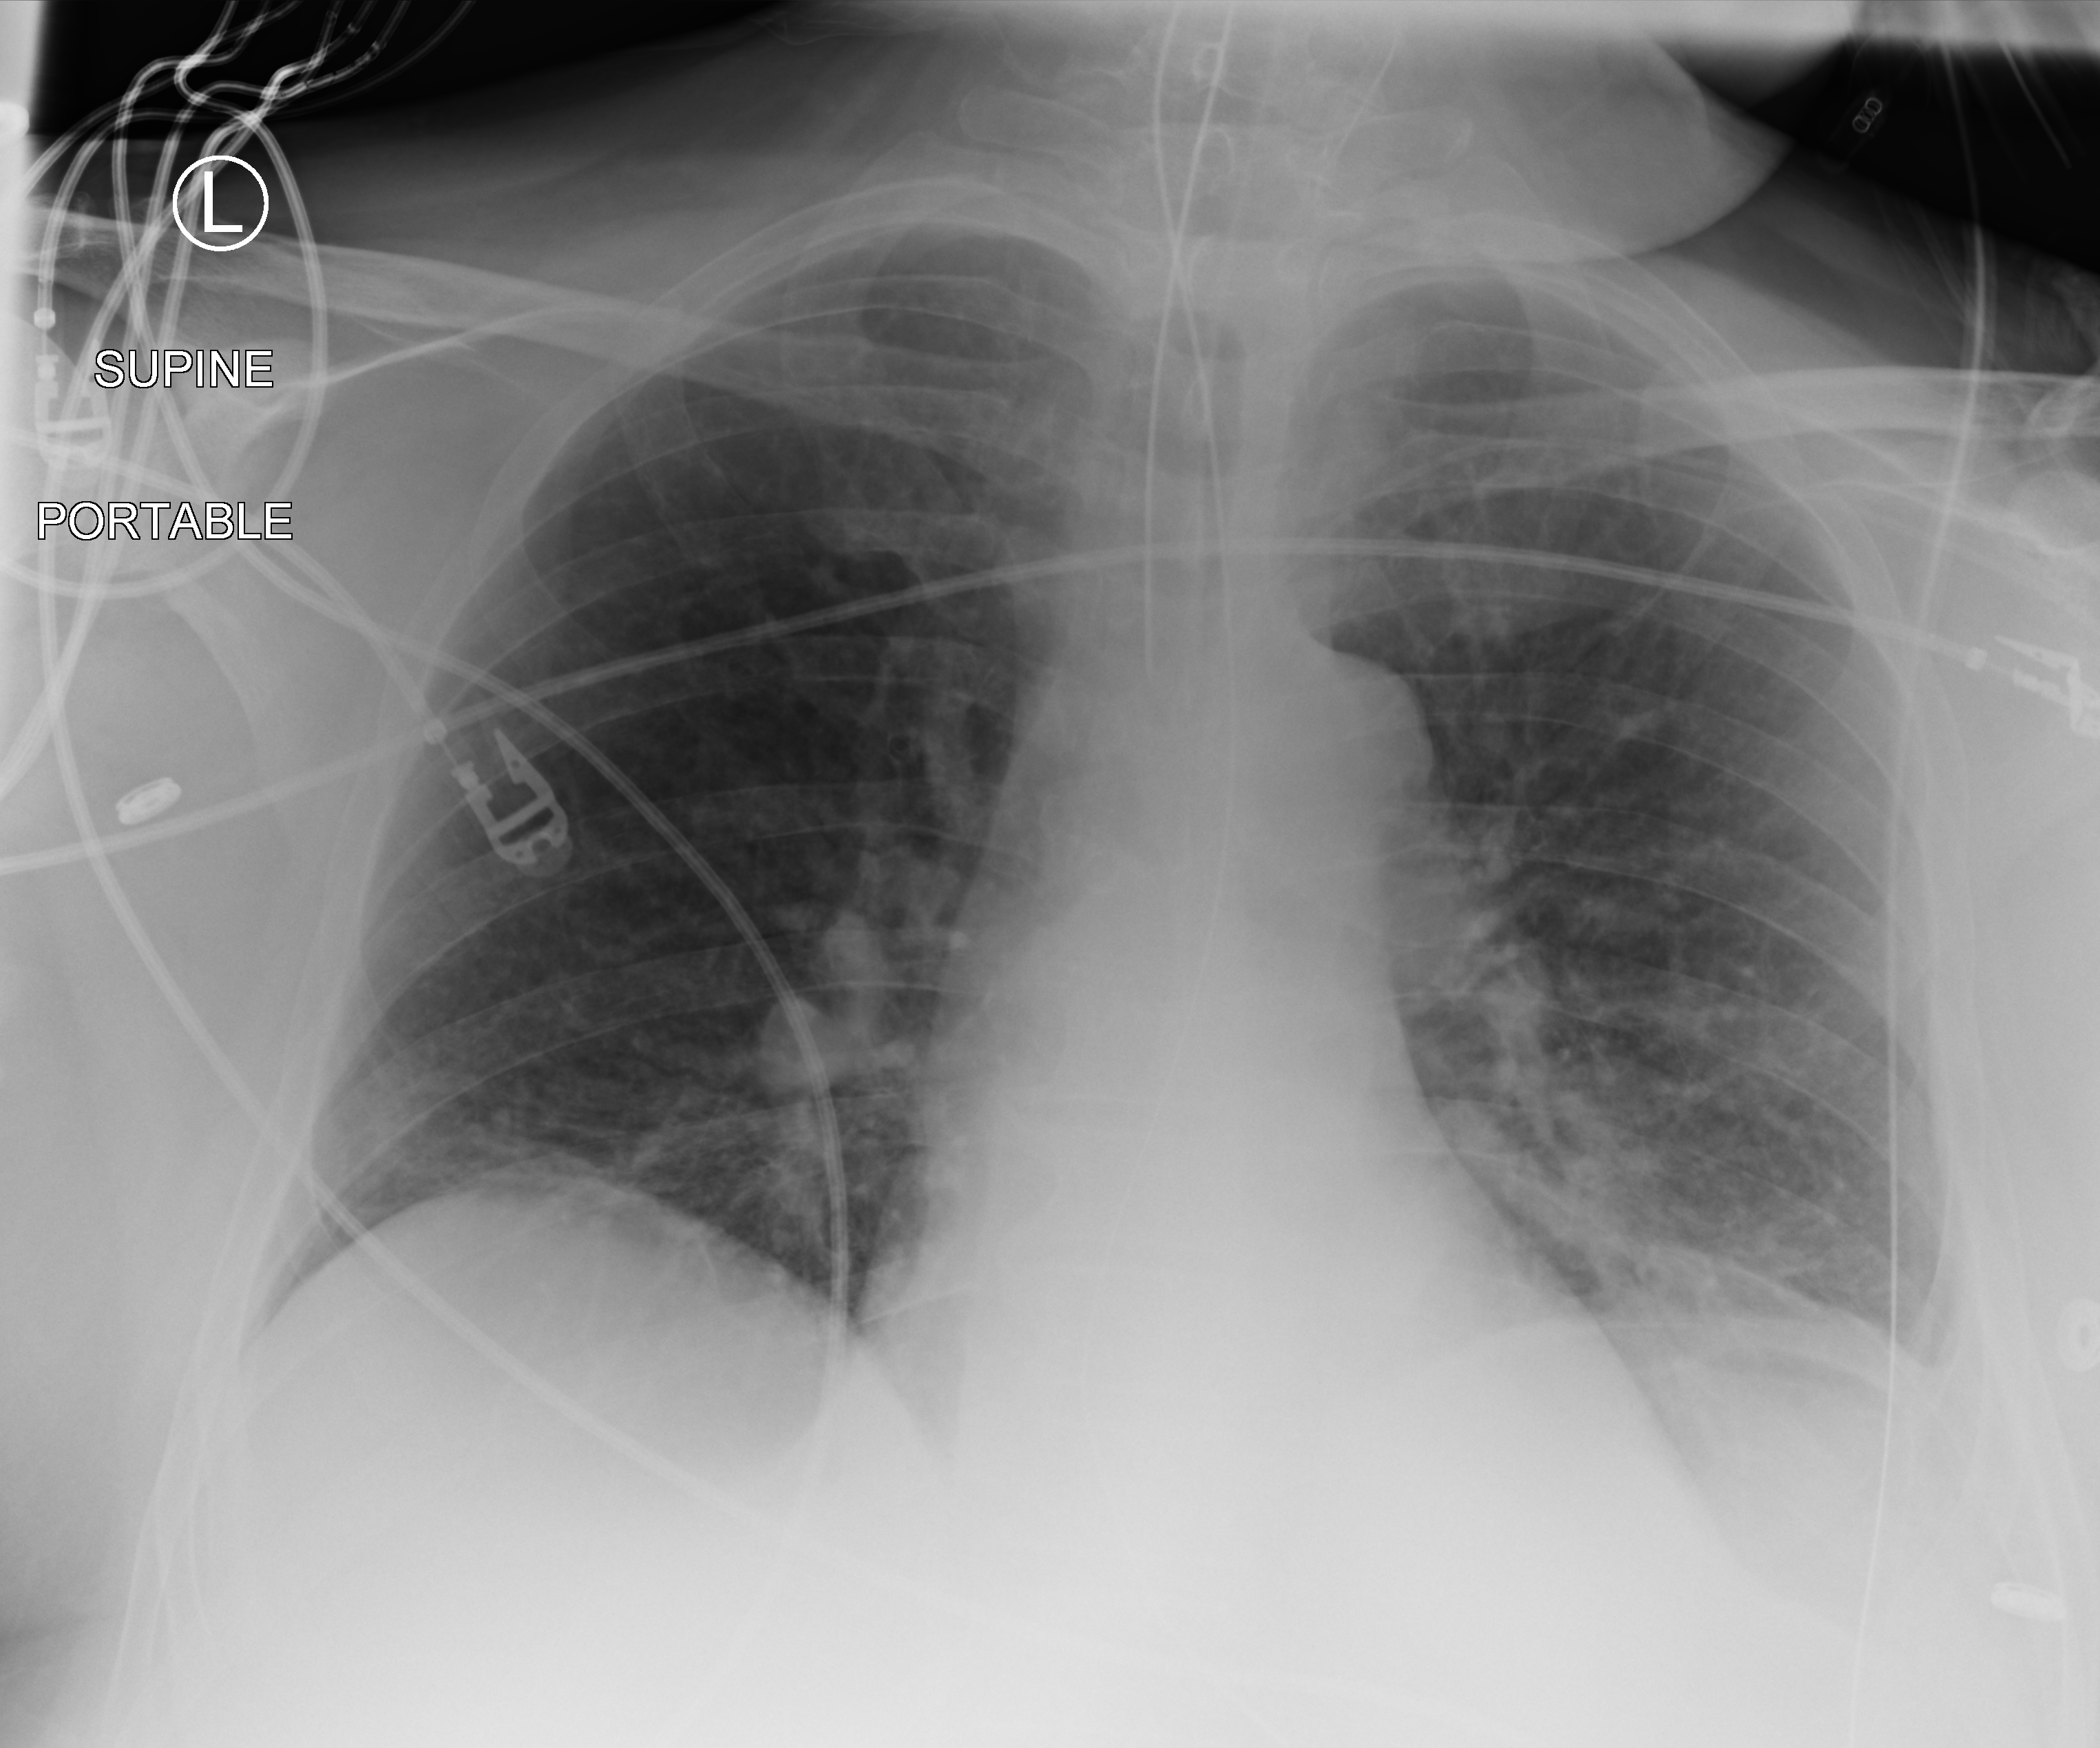
Portable chest radiograph; anteroposterior (AP) projection. Patient hospitalised with COVID-19; male, aged 60–74 years.
From the hospital-stay record, not from the radiograph (when in the stay this image was taken is not recorded): admitted to intensive care during this hospital stay: yes; chronic kidney disease (admission record): no; mechanically ventilated during this hospital stay: yes.